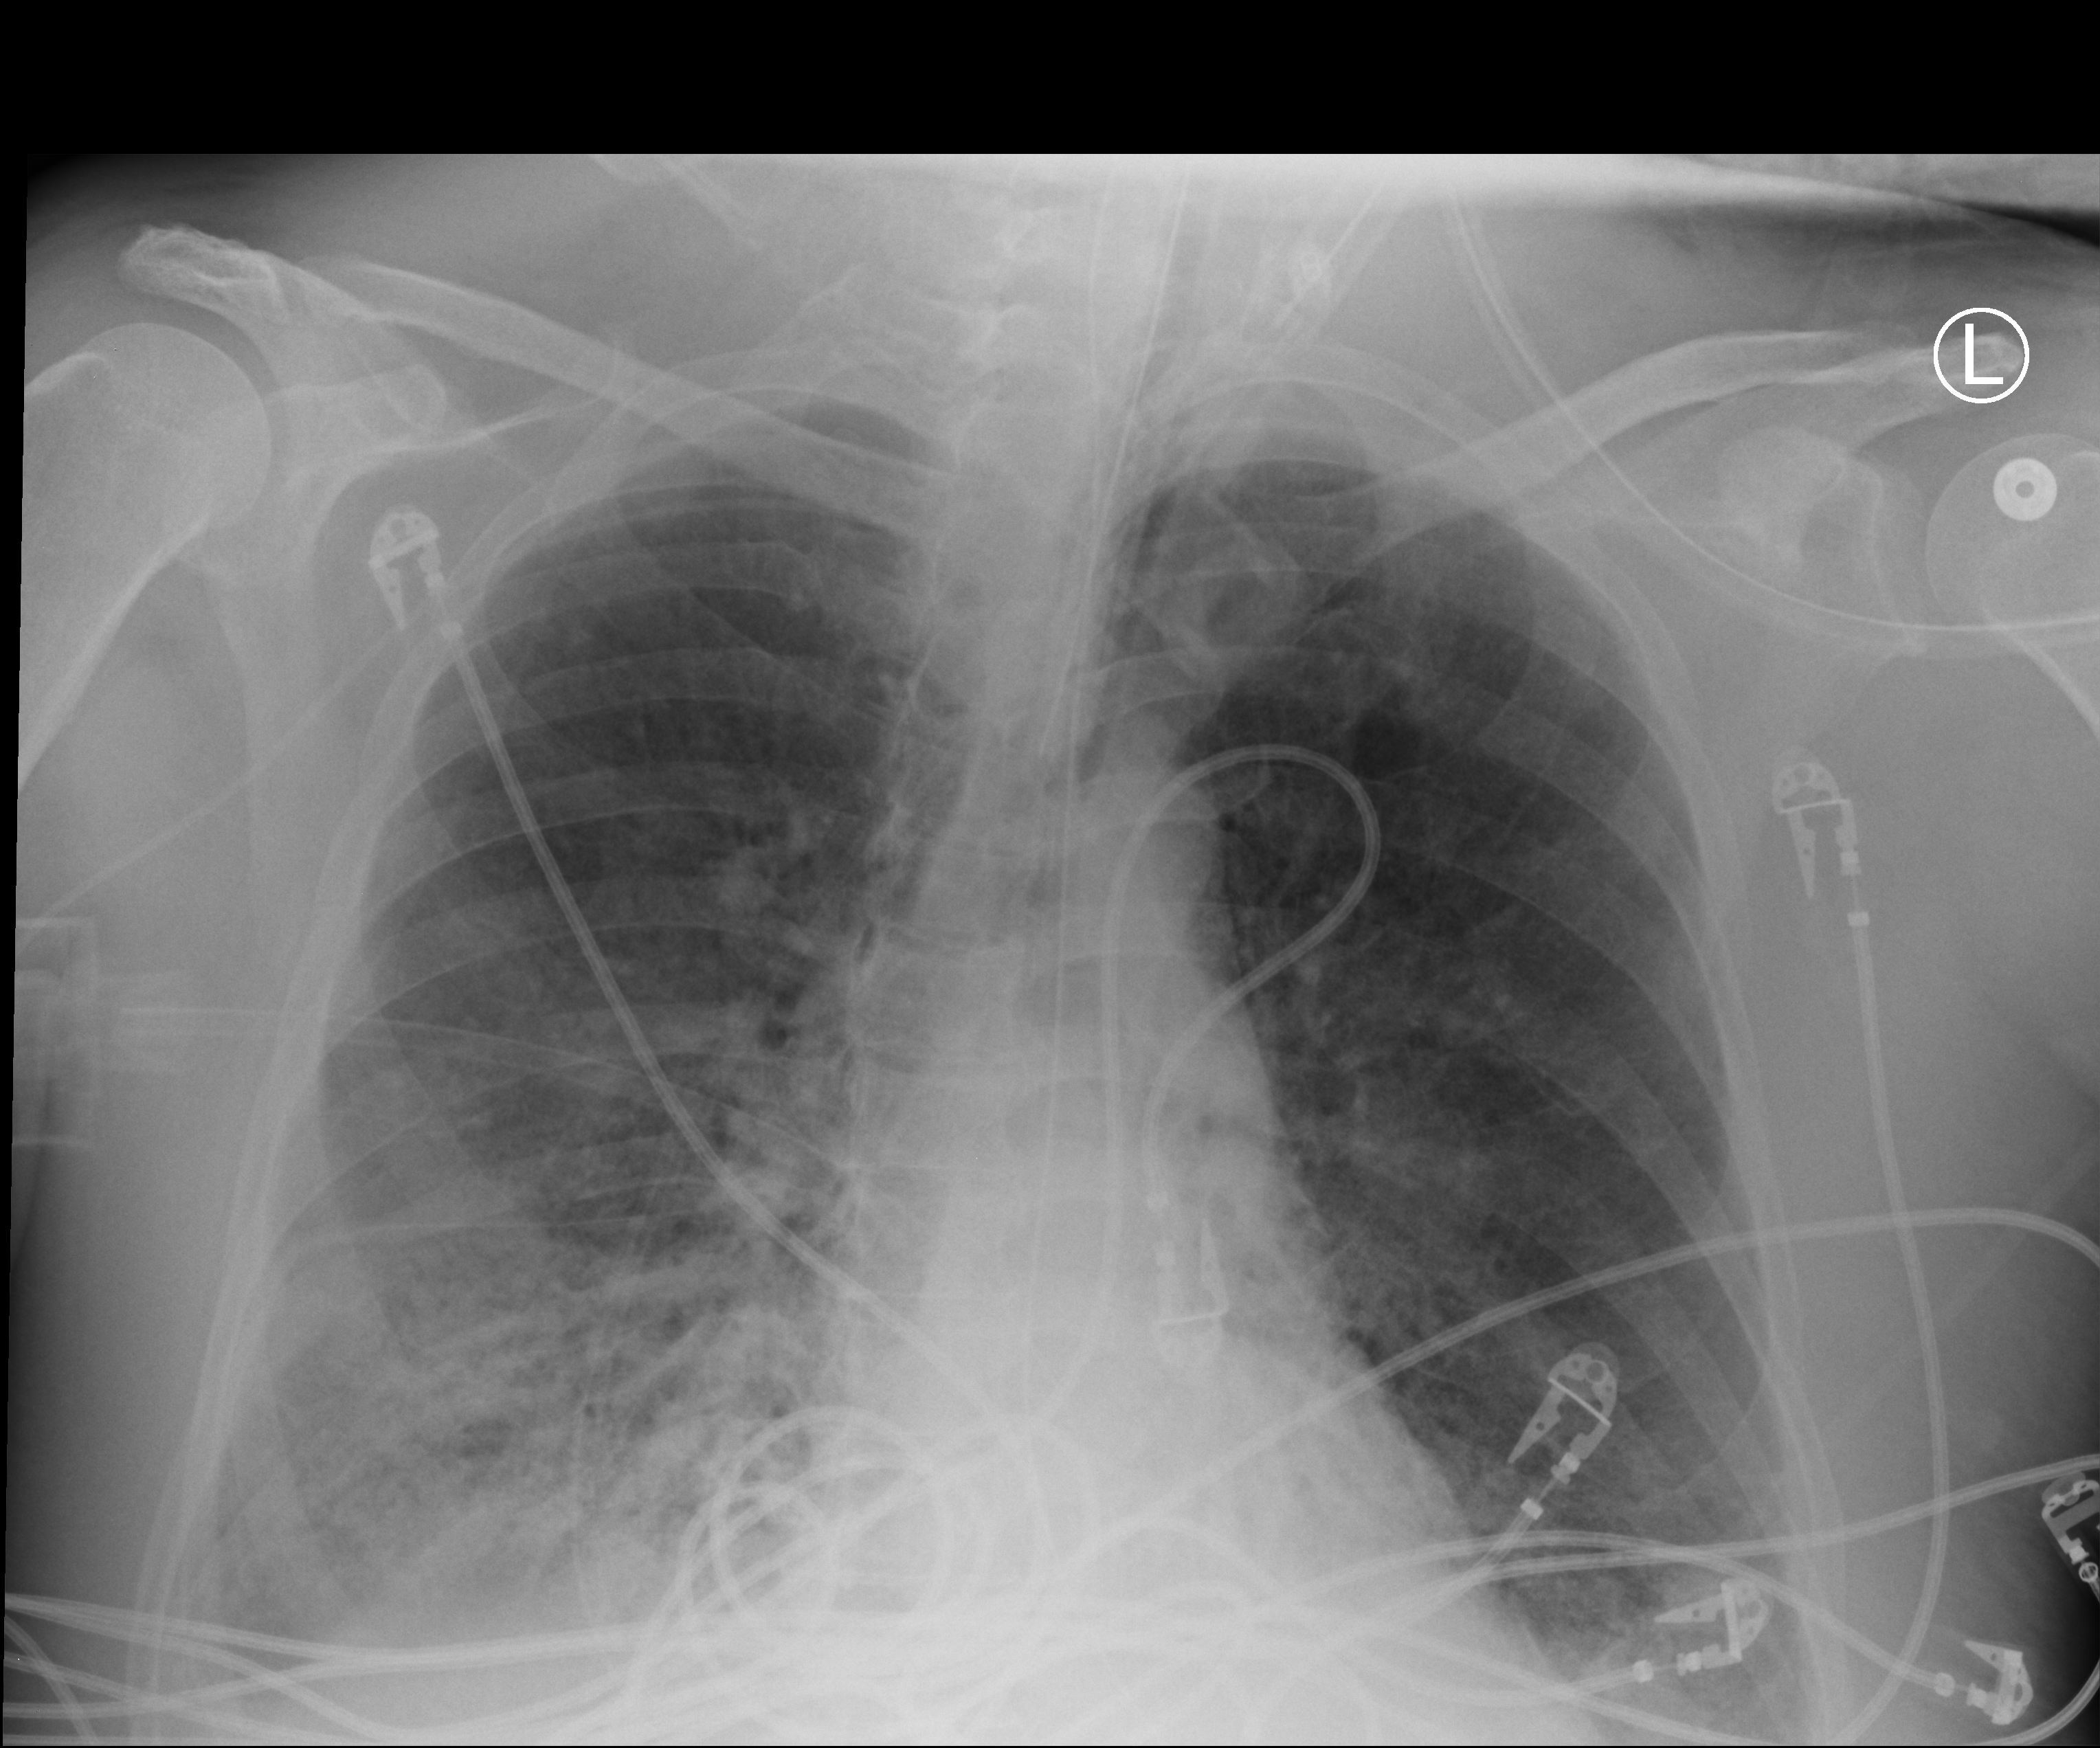
Portable chest radiograph; anteroposterior (AP) projection. Patient hospitalised with COVID-19; male, aged 60–74 years.
Admission-level facts for this patient (not findings on this image; timing relative to this image not recorded): COPD (admission record): no.